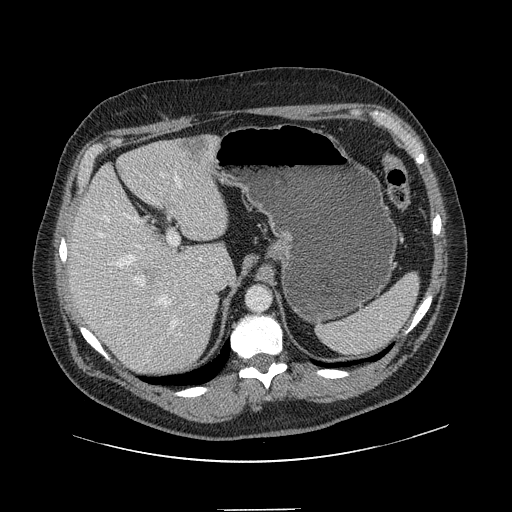
Contrast-enhanced abdominal CT, one axial slice; position 103 of 154 along the scan axis; intravenous contrast given; soft-tissue window (W 400 / L 40 HU); 512 × 512 image matrix. Male patient, age 61 years. From the clinical record (not read from this slice): diagnosis: colorectal cancer liver metastases, imaged before liver resection; multiple liver metastases: yes; largest metastasis: 2.6 cm; chemotherapy before resection: no.
Annotated regions visible in this slice (outlined manually by an expert reader):
- hepatic veins: bounding box [x1, y1, x2, y2] px = [98, 172, 181, 329]
- liver: [68, 137, 228, 377]
- planned liver remnant (the part of the liver to remain after resection): [68, 144, 228, 360]
- portal vein (with intrahepatic branches): [106, 172, 179, 285]
- liver metastasis: [183, 139, 206, 163]